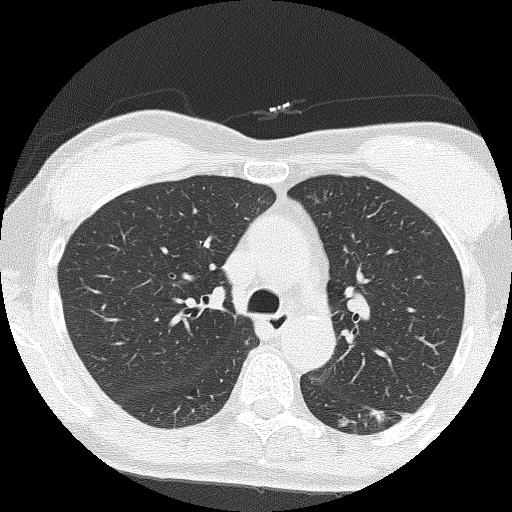
Low-dose screening chest CT, axial slice. Second screening round (one year after baseline). Lung window (W 1500 / L -600 HU). 2 mm slice thickness. 120 kVp. Female, age 64 years at enrolment. Former smoker at enrolment.
• Lesion marked by an expert reader, bounding box <353,394,413,440> (left, top, right, bottom; pixels).
• The screening reader recorded 3 non-calcified nodules or masses ≥4 mm on this exam; which of them this box marks is not recorded.